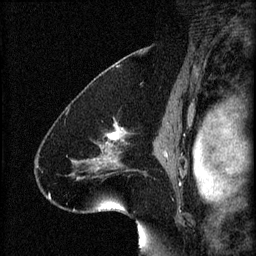
Breast MRI (dynamic contrast-enhanced), one sagittal slice; position 44 of 60 along the scan axis; 3 images stored at this slice position (order not interpretable as contrast timing); 1.5 T; TE 4.2 ms, TR 8.2 ms; 2 mm slice thickness; 256 × 256 image matrix. Female patient, age 41 years.
Outlined on this slice (semi-automatically segmented with operator editing):
- analysis volume of interest (the breast-tissue region the enhancement analysis was run in; not a lesion): bounding box (x1, y1, x2, y2) in pixels: (72, 120, 134, 181)
- tumour enhancement mask (voxels above the 70 % enhancement threshold inside the analysis volume of interest): (75, 124, 127, 163)